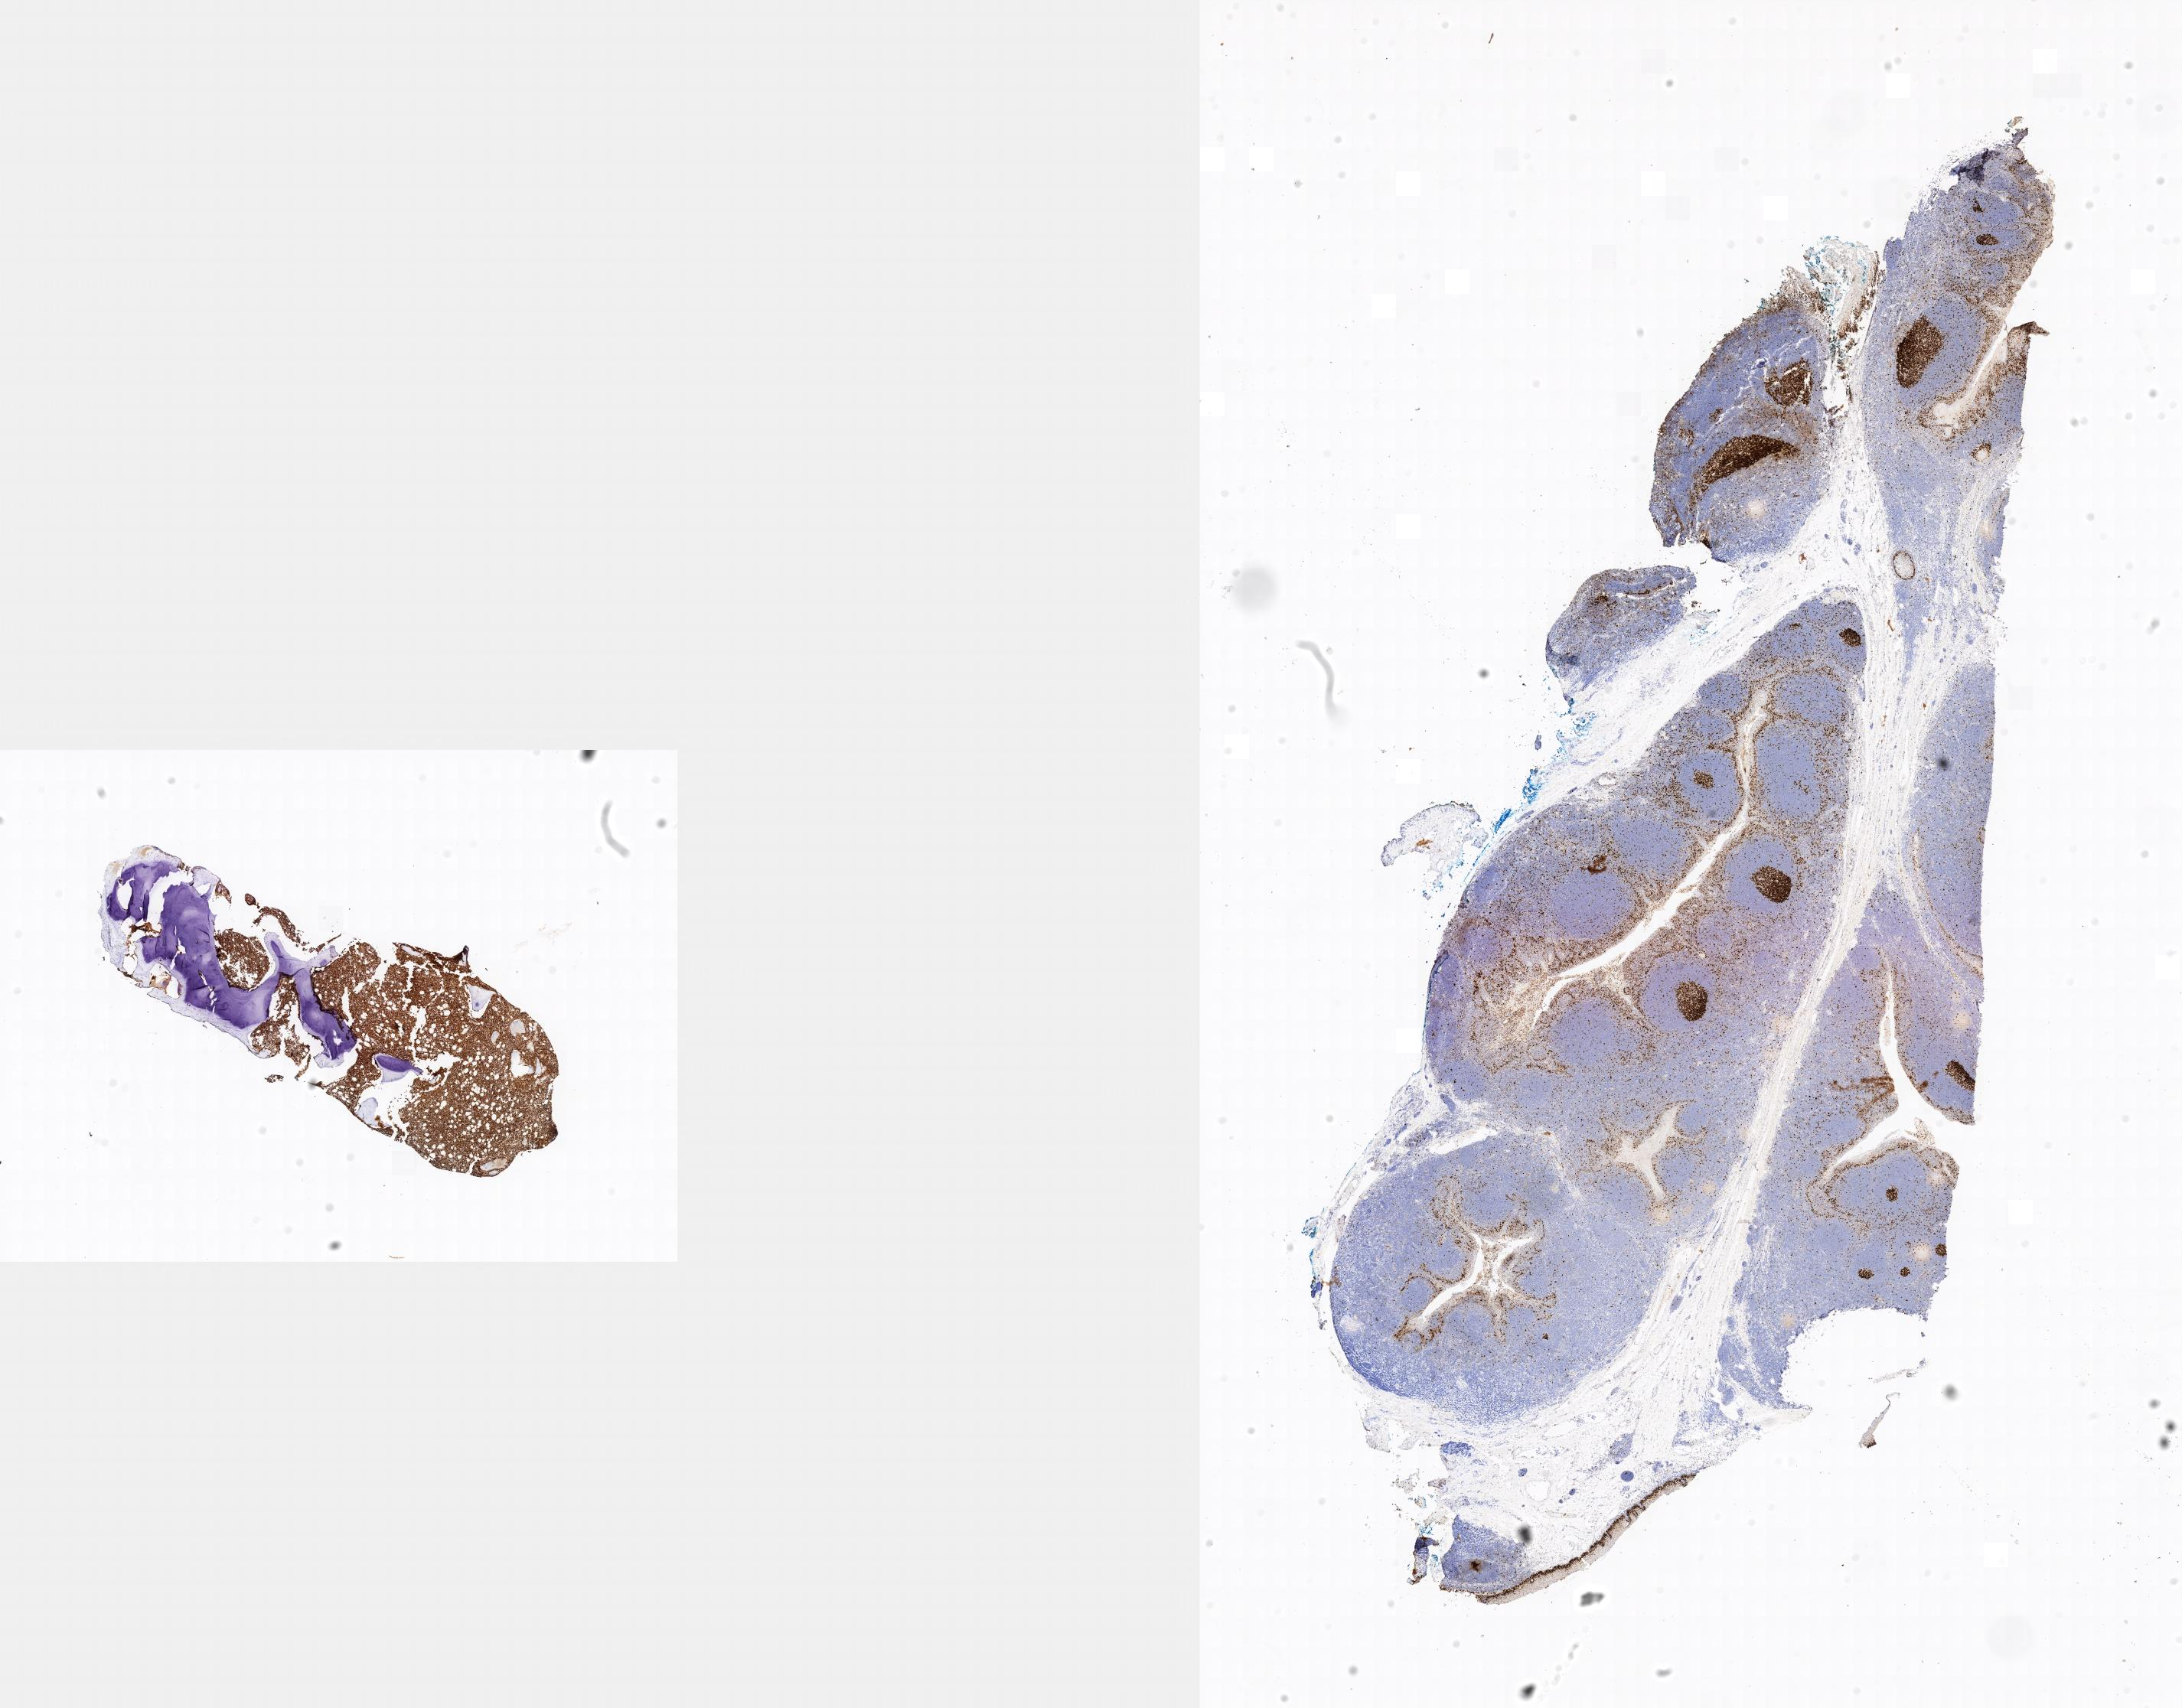
IHC for Ki-67, whole-slide image, whole scanned area shown as a low-resolution overview, specimen: tumor tissue, site: bone marrow. Male patient, age 15 years.
* histologic diagnosis: Burkitt lymphoma, NOS